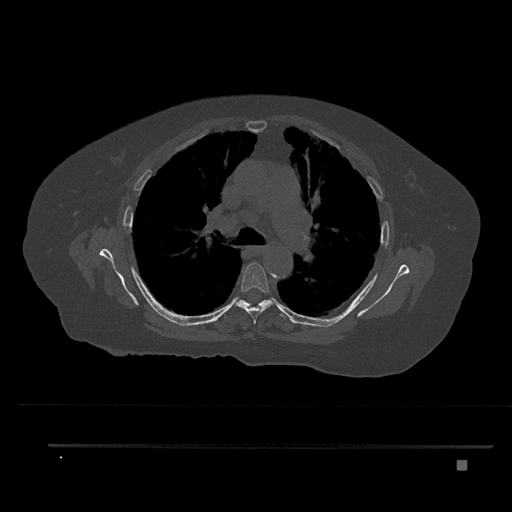
CT including the spine, one axial slice; slice 557 of 797 in the series (ordered by position); 120 kVp; bone window (W 1800 / L 400 HU); 0.5 mm slice thickness; 512 × 512 image matrix, field of view 437 × 437 mm. Female patient, age 76 years. Case-level facts recorded for this patient, not image findings: primary cancer: lung.
Annotated regions visible in this slice (semi-automatic segmentation, software-assisted and operator-edited):
- T5 vertebra: bounding box [x1, y1, x2, y2] px = [234, 262, 275, 324]
- T6 vertebra: [220, 299, 289, 317]